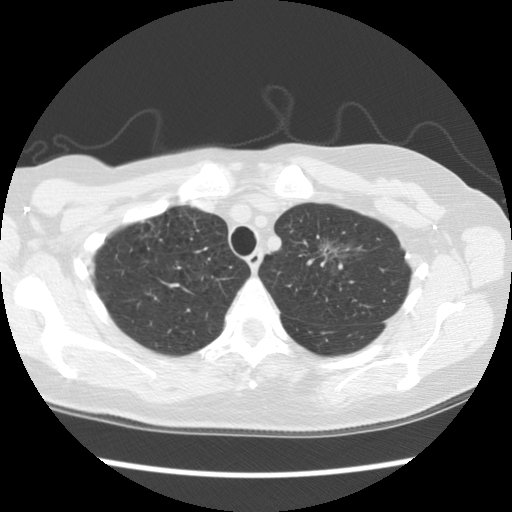
Axial slice from a low-dose chest CT screening exam; second screening round (one year after baseline); lung window (W 1500 / L -600 HU); slice 87 of 110 in the series. Female, age 65 years at enrolment. Former smoker at enrolment.
Expert reader's lesion annotation, box from (x=299, y=224) to (x=364, y=284) px. The screening reader recorded 2 non-calcified nodules or masses ≥4 mm on this exam (right upper lobe, left upper lobe); which of them this box marks is not recorded. Lung cancer was diagnosed 481 days after this screen (after the third annual screen): adenocarcinoma, NOS, left upper lobe, moderately differentiated (G2), stage IA (AJCC 6th edition), 30 mm at pathology.